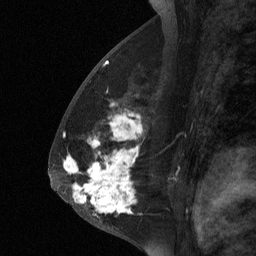
Breast MRI (dynamic contrast-enhanced), one sagittal slice. Slice 36 of 64 in the series (ordered by position). Dynamic contrast-enhanced study with each time point stored as its own series, time point 2 of 3 at this slice position (early post-contrast, ordered by acquisition time). 1.5 T. TE 4.8 ms, TR 27 ms. 2 mm slice thickness. 256 × 256 image matrix, field of view 180 × 180 mm. Female patient, age 56 years. From the clinical record (not read from this slice): setting: breast cancer imaged before/during neoadjuvant chemotherapy; receptor status: HER2-positive.
Annotated regions visible in this slice (semi-automatic segmentation, software-assisted and operator-edited):
- analysis volume of interest (the breast-tissue region the enhancement analysis was run in; not a lesion): bounding box (x1, y1, x2, y2) in pixels: (59, 104, 142, 229)
- tumour enhancement mask (voxels above the 90 % enhancement threshold inside the analysis volume of interest): (65, 160, 132, 212)